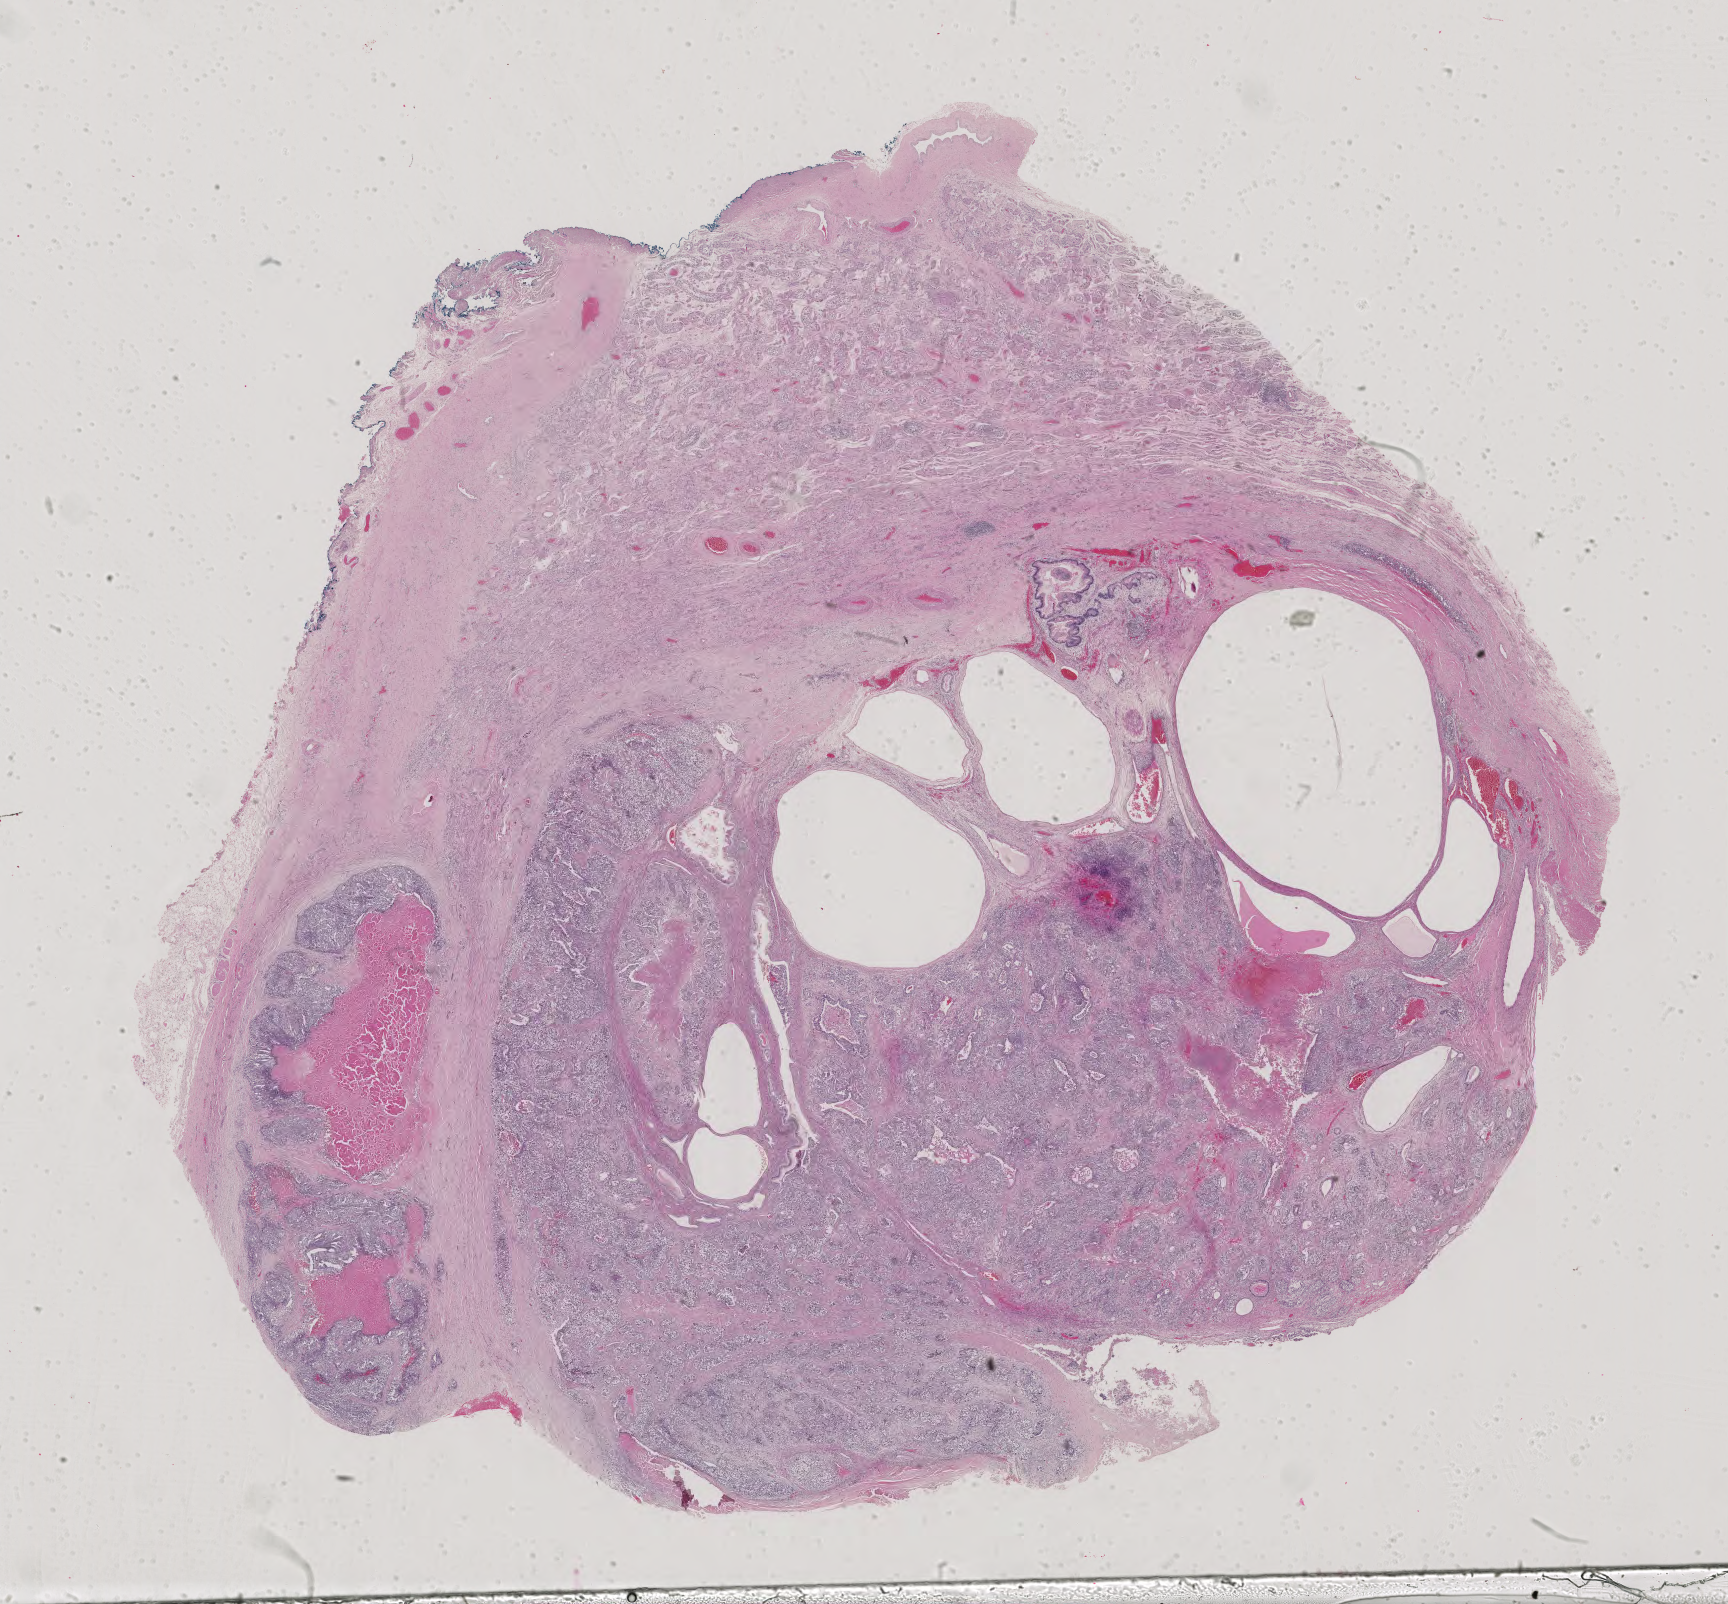
H&E-stained whole-slide image, shown as a low-resolution overview of the whole scanned area (about 25.2 x 23.4 mm, acquisition: 40x scan). Formalin-fixed paraffin-embedded (FFPE) diagnostic section. Testis, primary tumour sample. Male patient; age at initial diagnosis 25 years.
TNM: T2 N1 M0. Histologic diagnosis: Seminoma, NOS. AJCC pathologic stage: IIIB (6th edition).